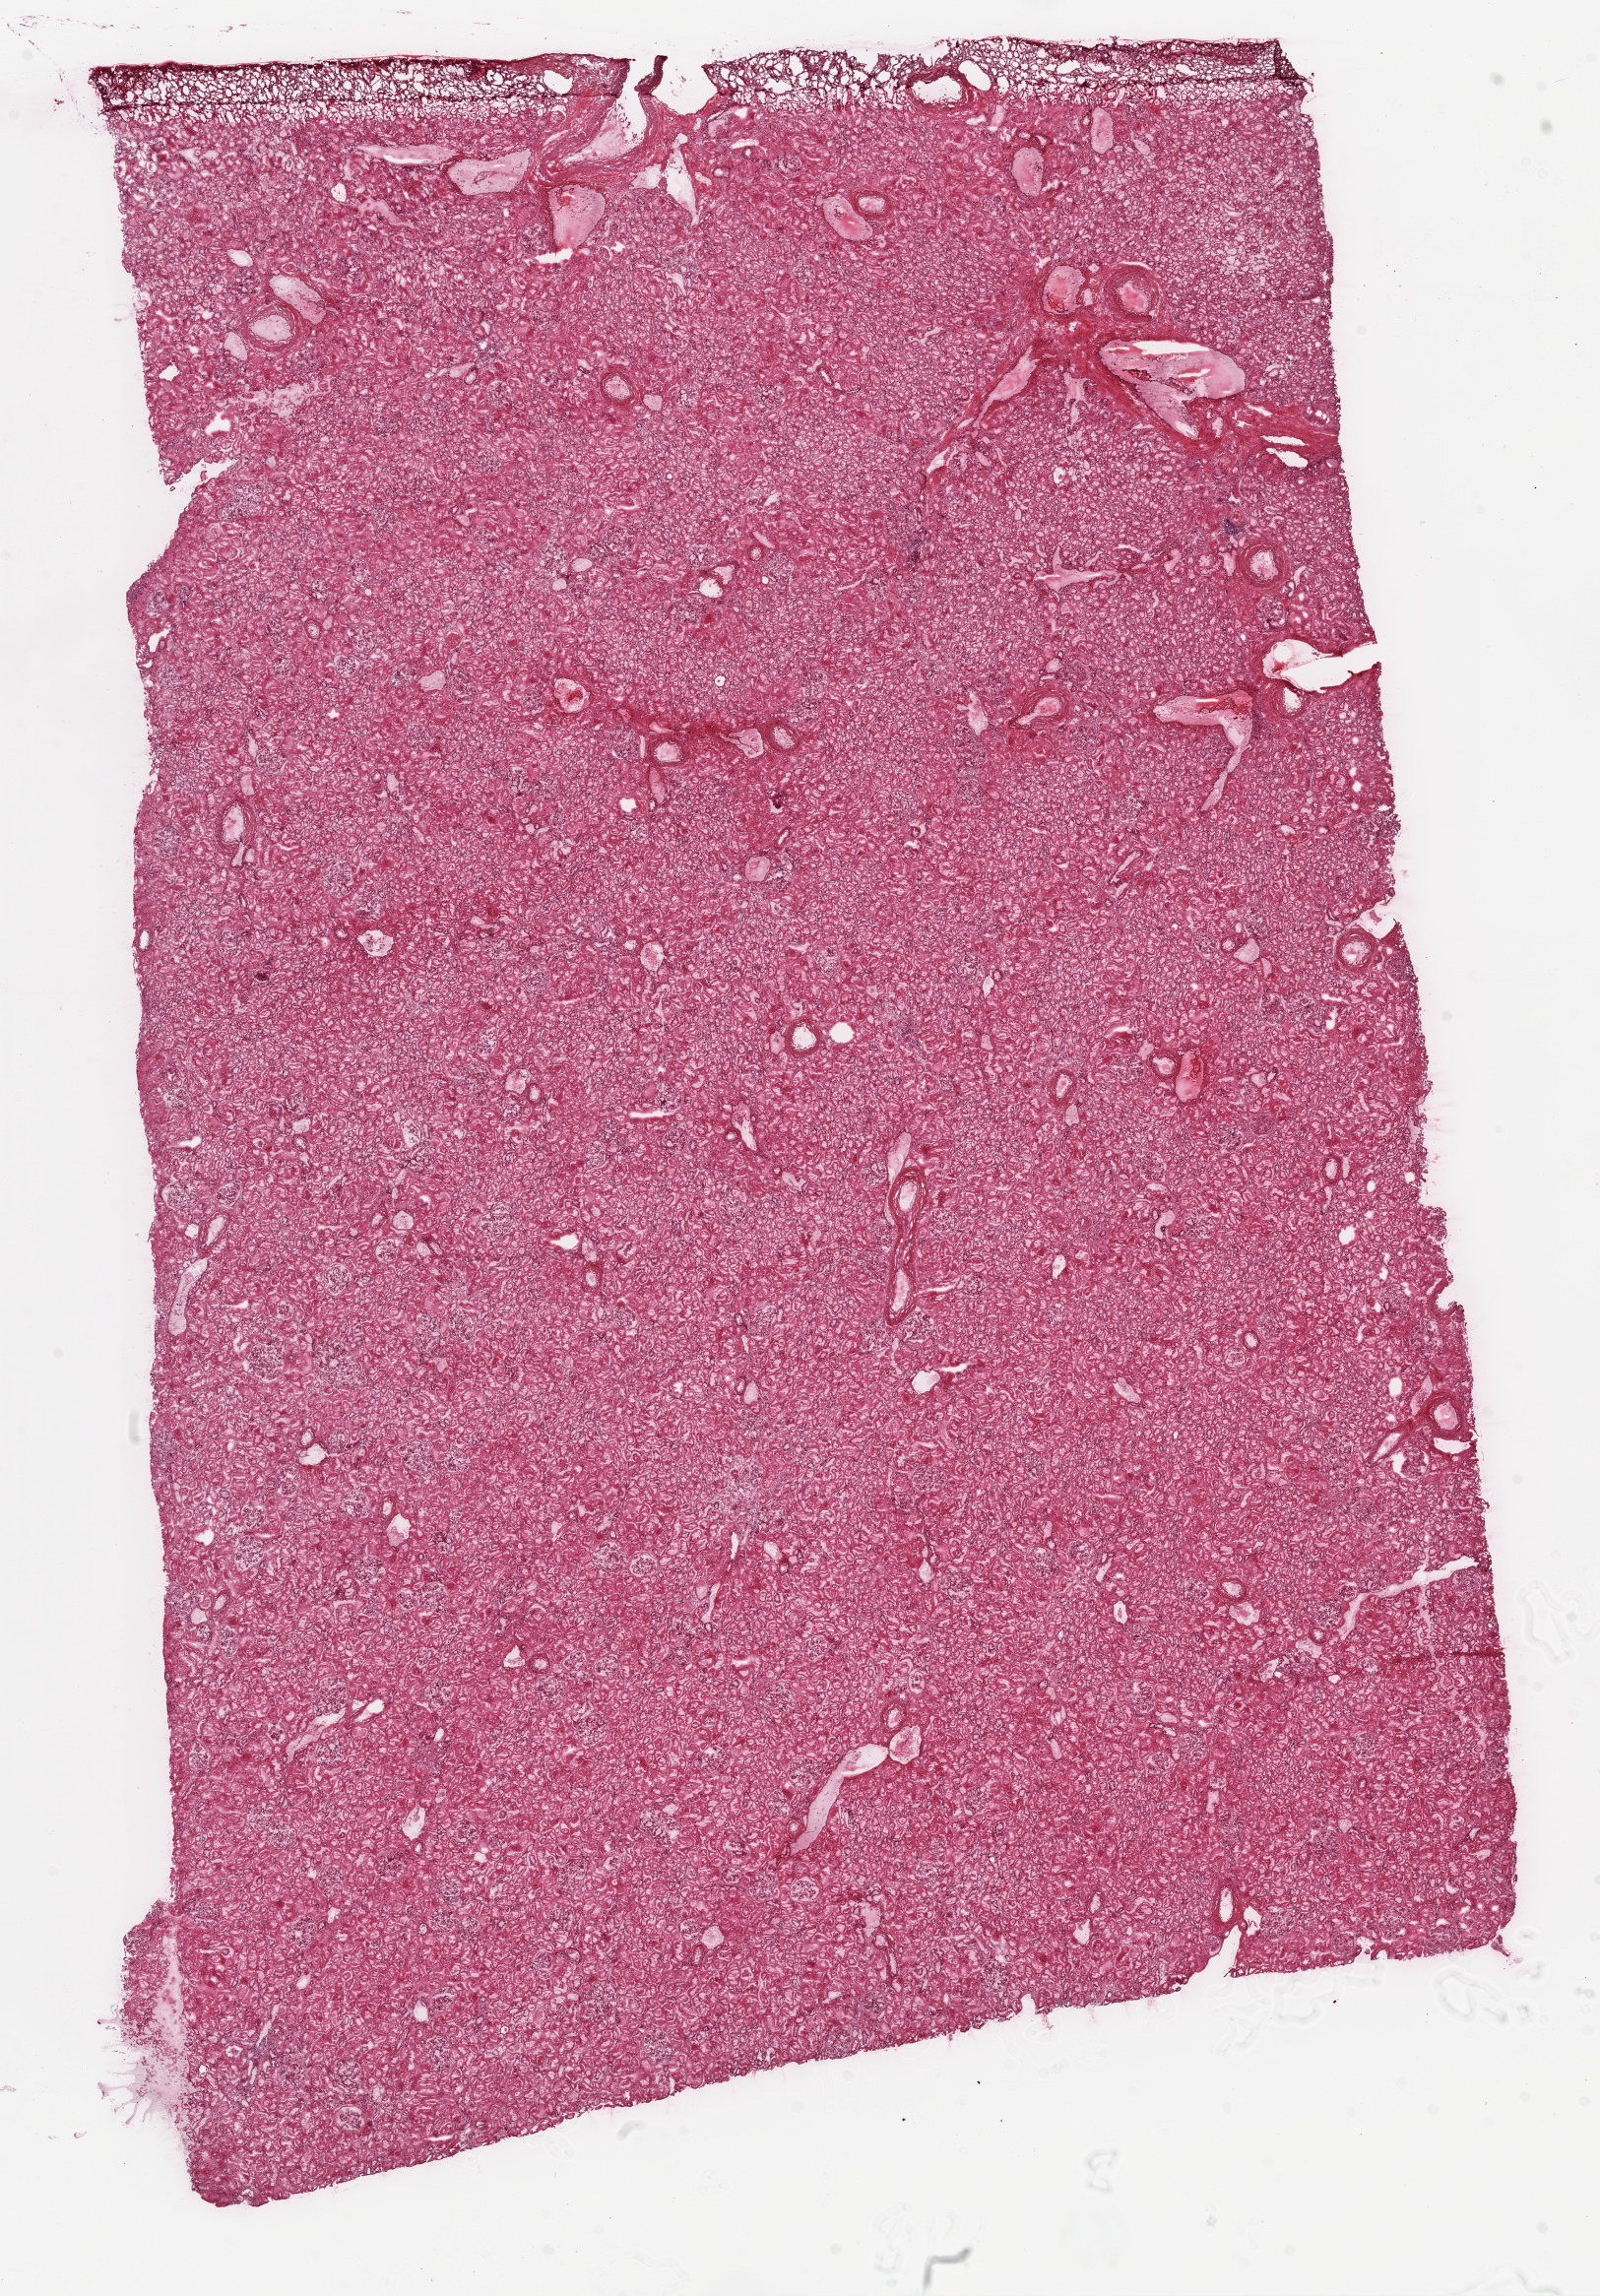
H&E-stained whole-slide image — low-resolution overview of the scanned area, about 13.0 x 18.7 mm (from a 20x scan). Frozen section from the top of the tissue portion. Sample: solid tissue normal (non-tumour tissue), kidney. Patient: male, age at initial diagnosis 63 years.
• this section: solid tissue normal (non-tumour) sample from the same patient
• patient diagnosis: Clear cell adenocarcinoma, NOS